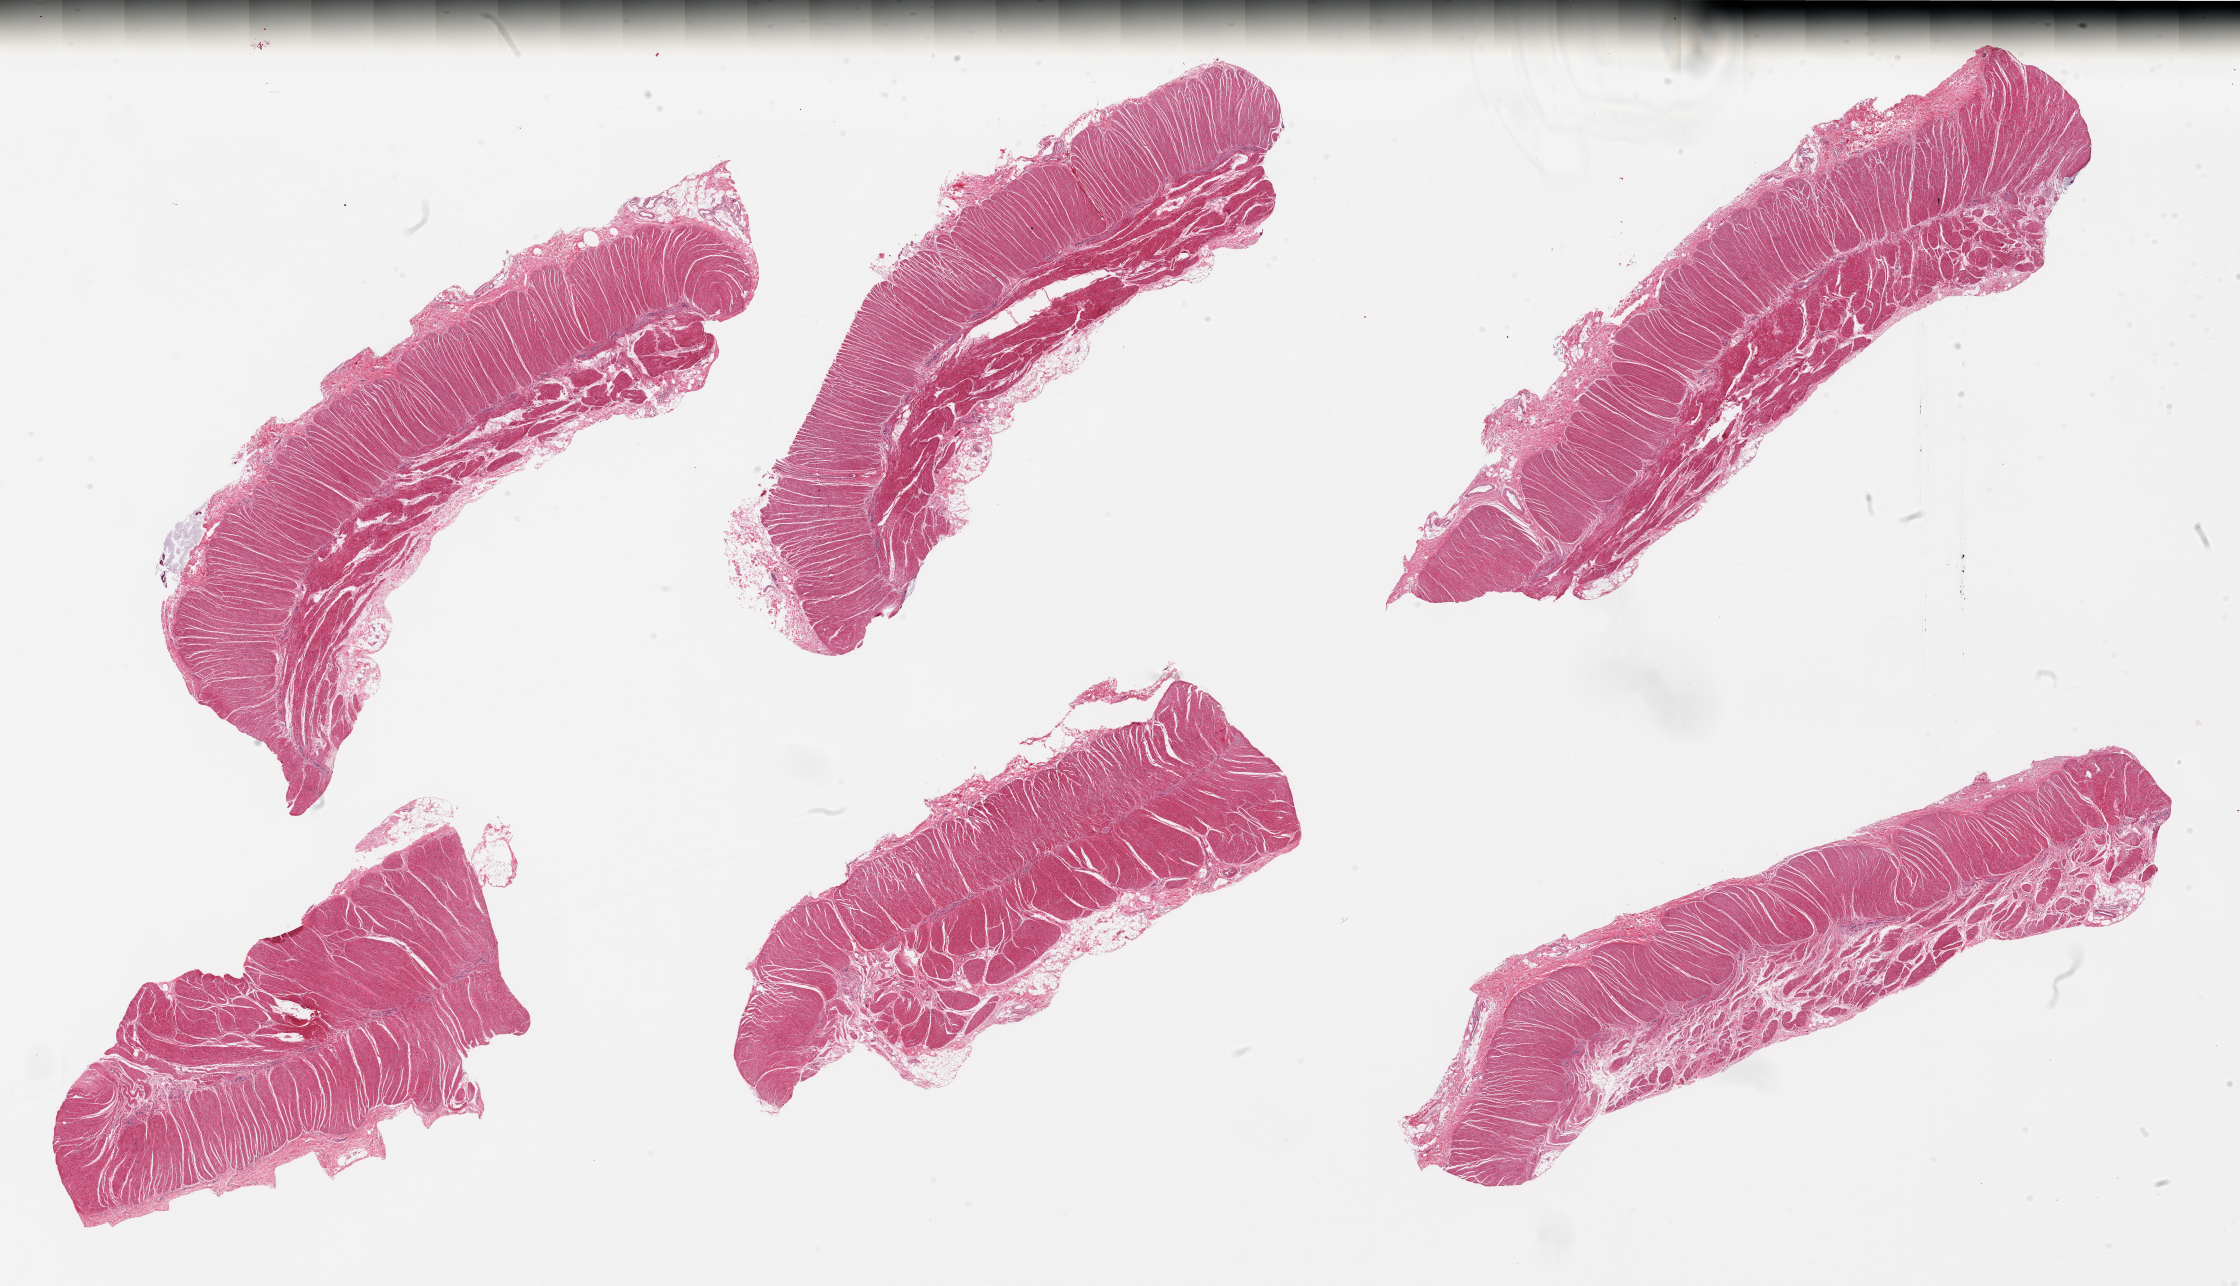
Hematoxylin and eosin (H&E) whole-slide image, brightfield — a low-resolution overview of the entire scanned area, about 35.4 x 20.3 mm (from a 20x scan), PAXgene-fixed, paraffin-embedded tissue, section of sigmoid colon (target tissue), tissue donor sample. Male donor.
Pathologist's review note for this sample: 6 pieces; relatively well trimmed with some residual attached fat.